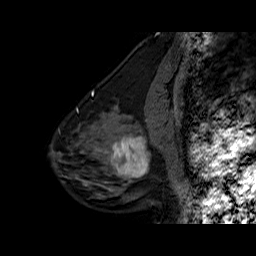
Breast MRI (dynamic contrast-enhanced), one sagittal slice. Position 22 of 60 along the scan axis. Dynamic contrast-enhanced series, time point 2 of 6 at this slice position (early post-contrast). 1.5 T. TE 6.3 ms, TR 32.5 ms. 4 mm slice thickness. 256 × 256 image matrix, field of view 200 × 200 mm. Female patient. Case-level facts recorded for this patient, not image findings: setting: breast cancer imaged before/during neoadjuvant chemotherapy; receptor status: triple-negative.
Outlined on this slice (semi-automatically segmented with operator editing):
- analysis volume of interest (the breast-tissue region the enhancement analysis was run in; not a lesion): bounding box <102,127,162,186> (left, top, right, bottom; pixels)
- tumour enhancement mask (voxels above the 100 % enhancement threshold inside the analysis volume of interest): <111,136,150,177>